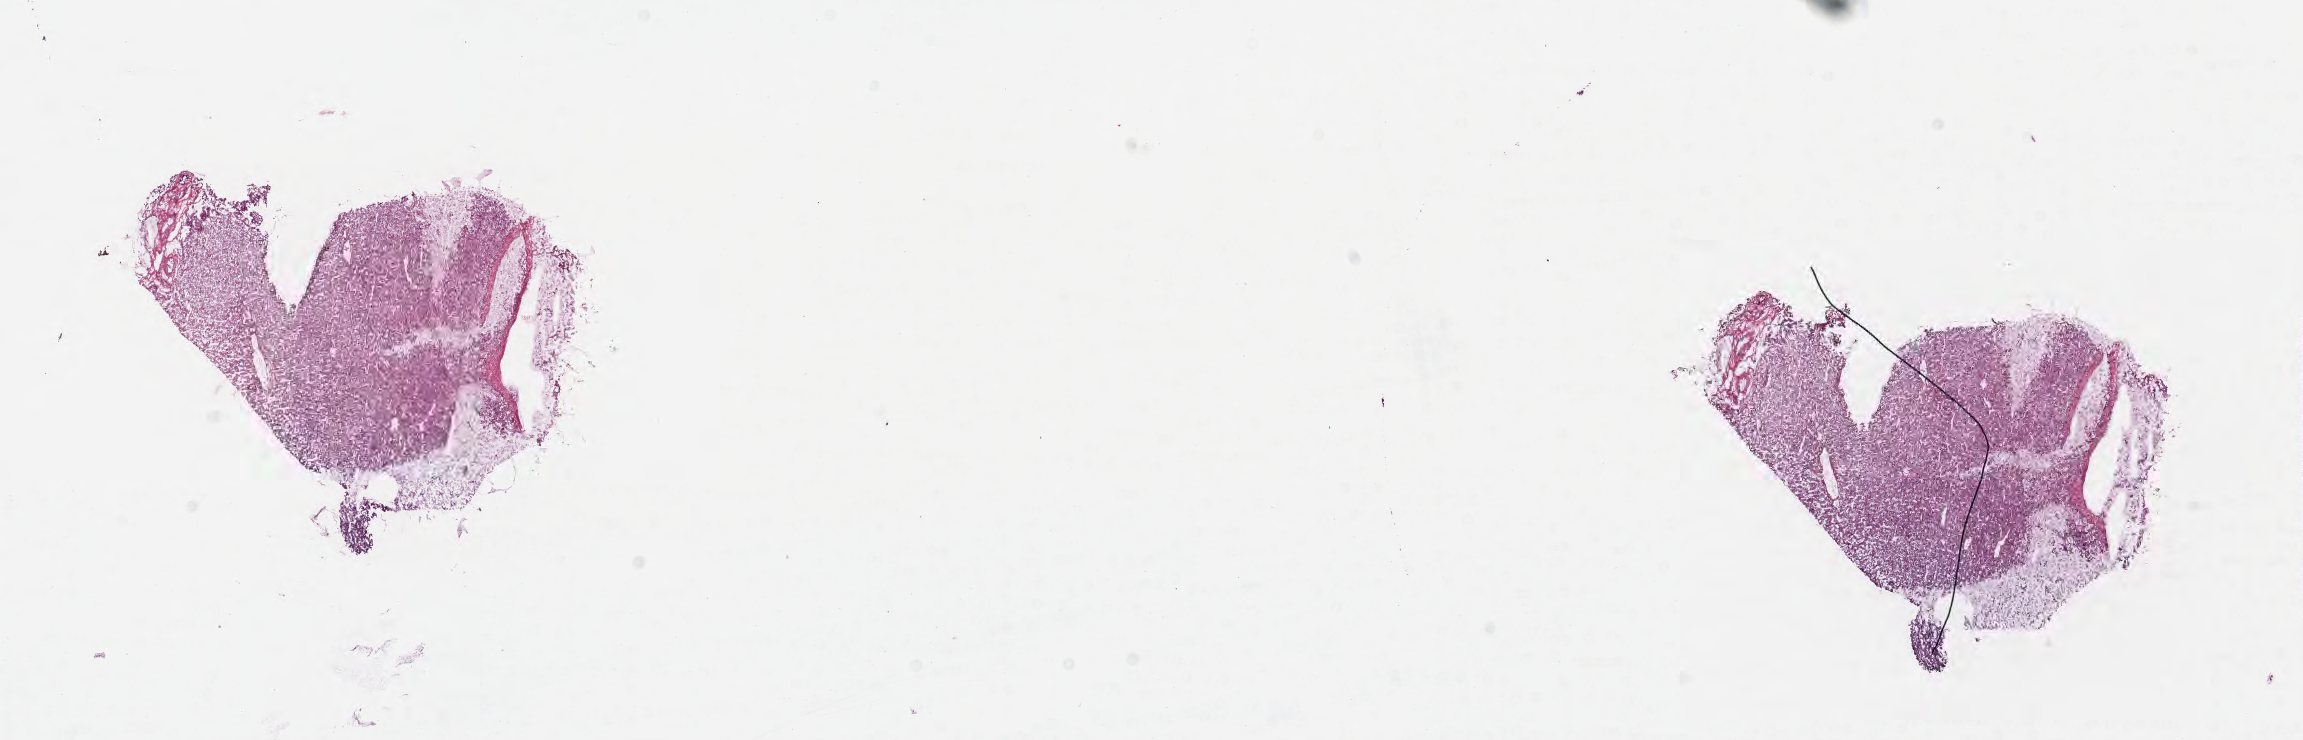
Whole-slide image, haematoxylin and eosin stain, whole scanned area (about 18.6 x 6.0 mm) shown as a low-resolution overview, frozen section, specimen: normal-tissue sample (non-tumor) from a patient with adenocarcinoma, NOS, anatomic site: liver. Female patient; age at initial diagnosis 51 years. Pathologist review of this section (percent, as recorded): tumor cells 0%, tumor nuclei 0%, stromal cells 25%, necrosis 0%, normal cells 75%. Inflammatory infiltration, as recorded: lymphocyte infiltration 1%, monocyte infiltration 1%, neutrophil infiltration 0%.
• this section: non-tumor tissue sample; the patient's diagnosis is given above
• section: top of the tissue portion